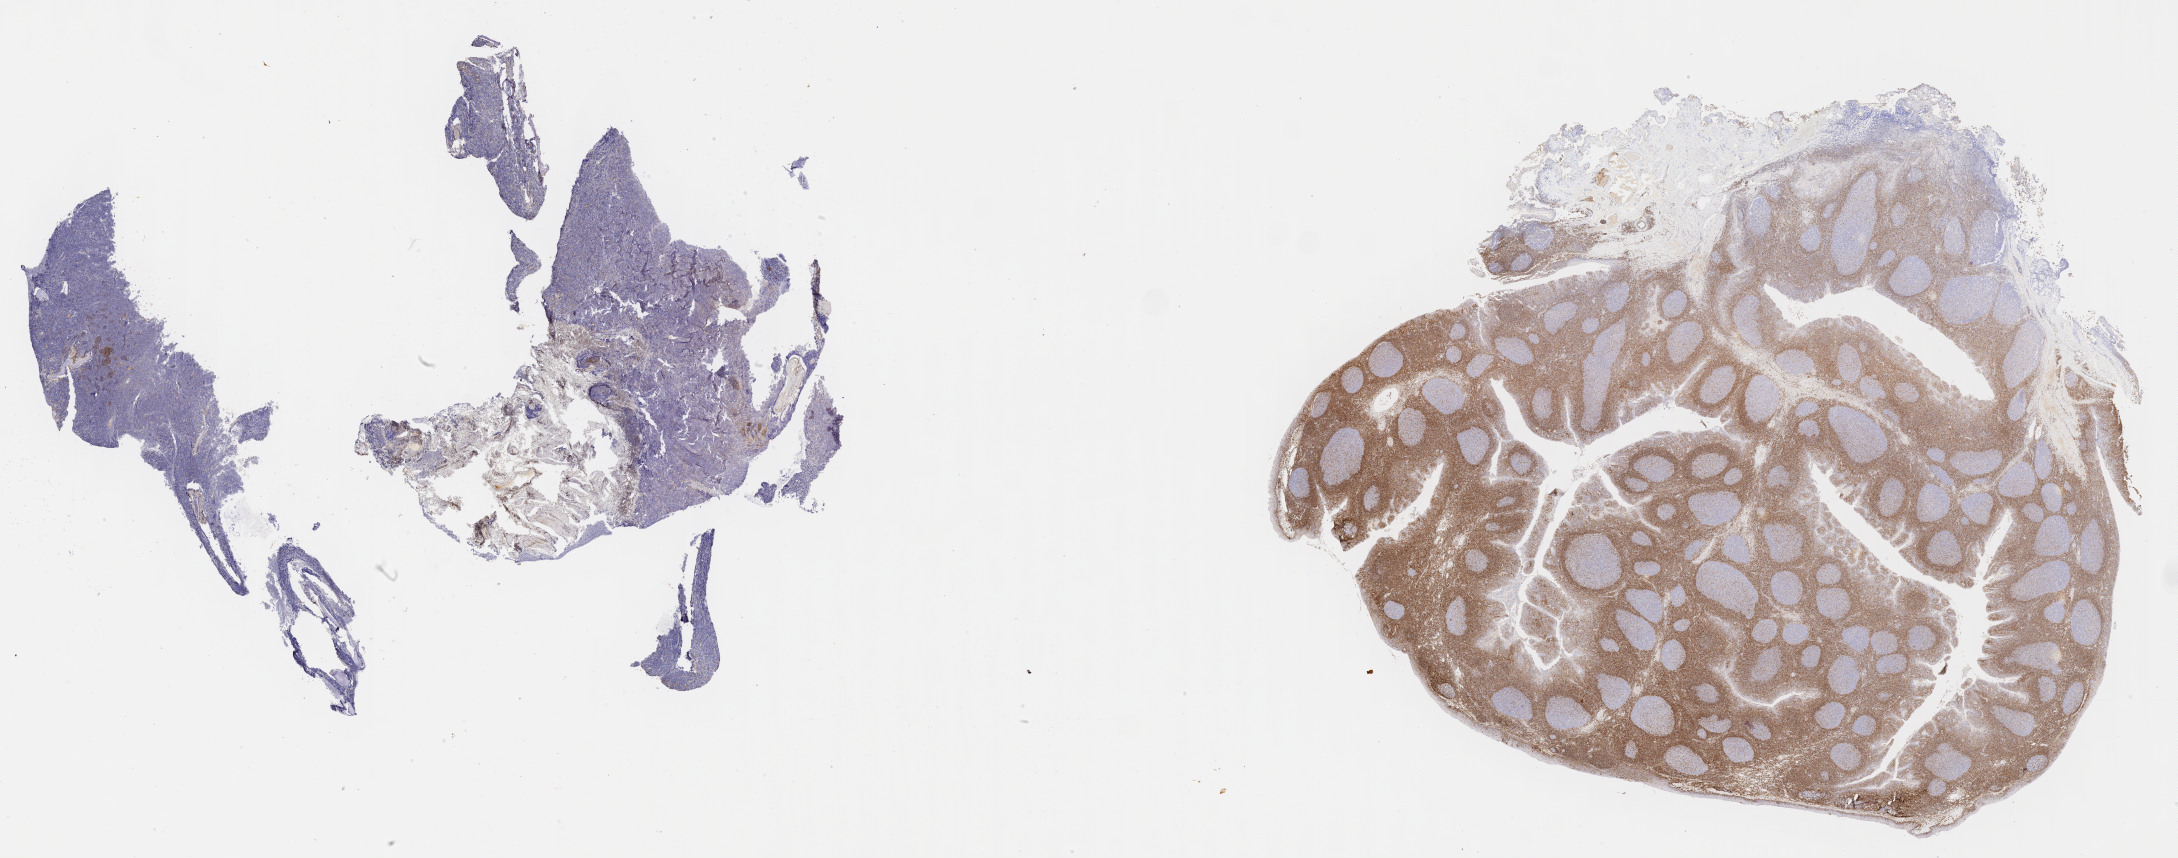
Whole-slide image, immunohistochemical stain for BCL2 — shown as a low-resolution overview of the whole scanned area (about 35.2 x 13.9 mm), tumor tissue, site: cranium. Male, age 8 years at initial diagnosis.
- histologic diagnosis: Burkitt lymphoma, NOS